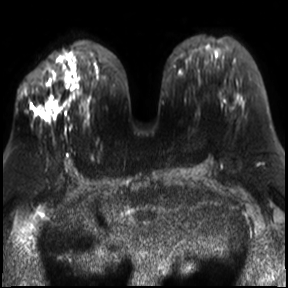
Breast MRI, one axial slice; diffusion-weighted series; image 2 of 4 stored at this slice position (different b-values; order by instance number); 3 T; 288 × 288 image matrix. Female patient.
Outlined on this slice (outlined manually by an expert reader):
- tumour on diffusion-weighted imaging: bounding box [x1, y1, x2, y2] px = [41, 70, 70, 120]